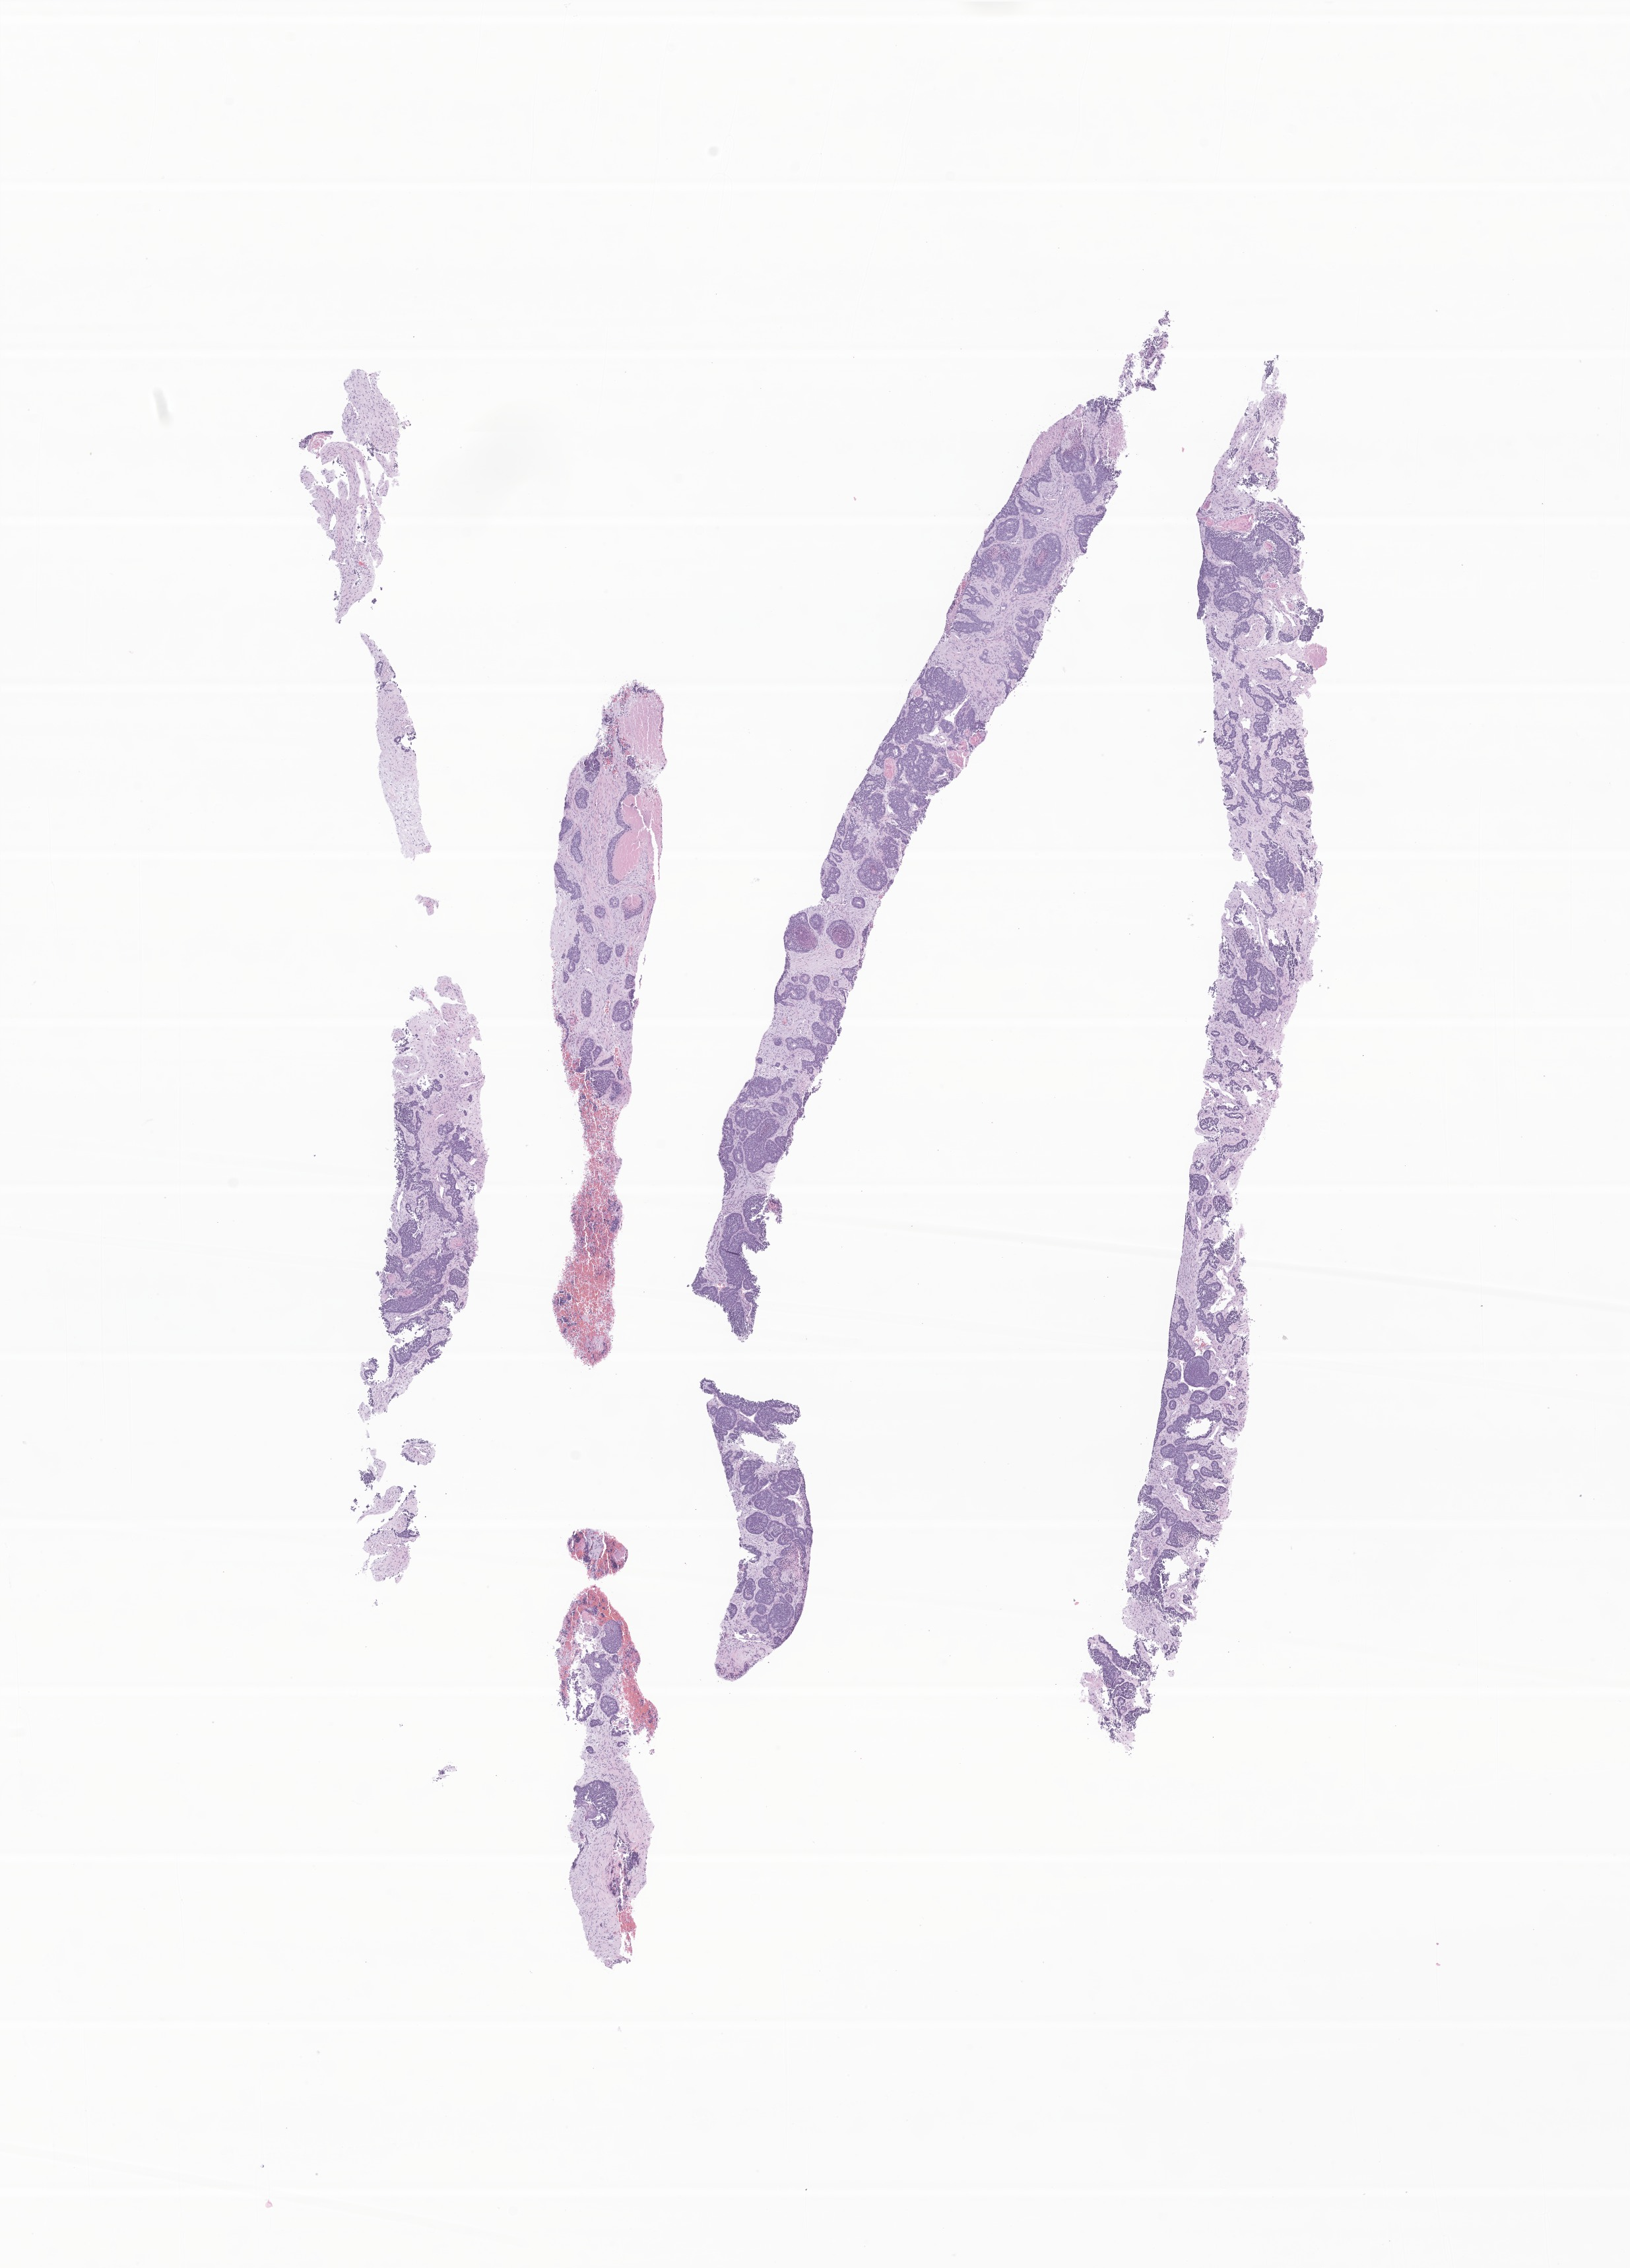
Digitized haematoxylin and eosin-stained section of tumor tissue — shown as a low-resolution overview of the whole scanned area (about 10.4 x 14.5 mm); FFPE section. Male patient, age 105 months (8 years 9 months).
Diagnosis (ICD-O-3 morphology term): Carcinoma, metastatic, NOS.